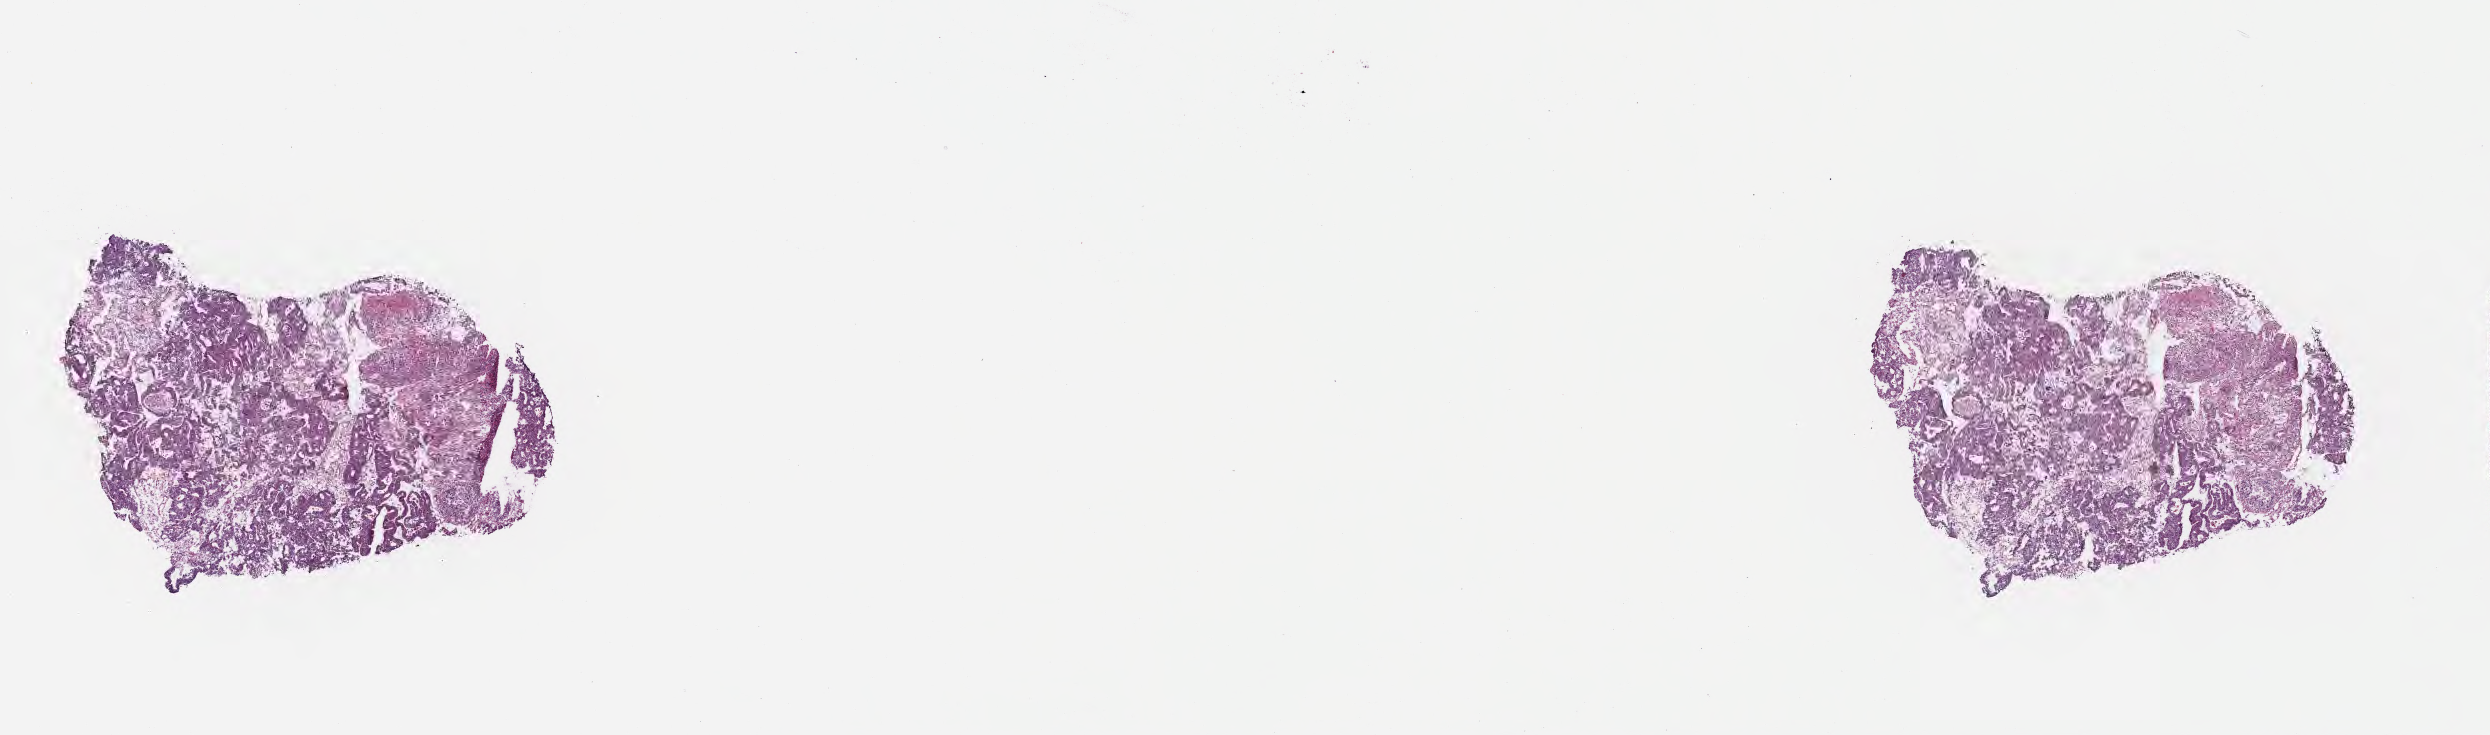
Whole-slide image, H&E stain, whole scanned area (about 20.1 x 5.9 mm) shown as a low-resolution overview. Cryosection. Specimen: primary tumor. Site: sigmoid colon. Female, age 60 years at initial diagnosis. Pathologist review of this section (percent, as recorded): tumor cells 80%, tumor nuclei 80%.
Diagnosis: Adenocarcinoma, NOS.